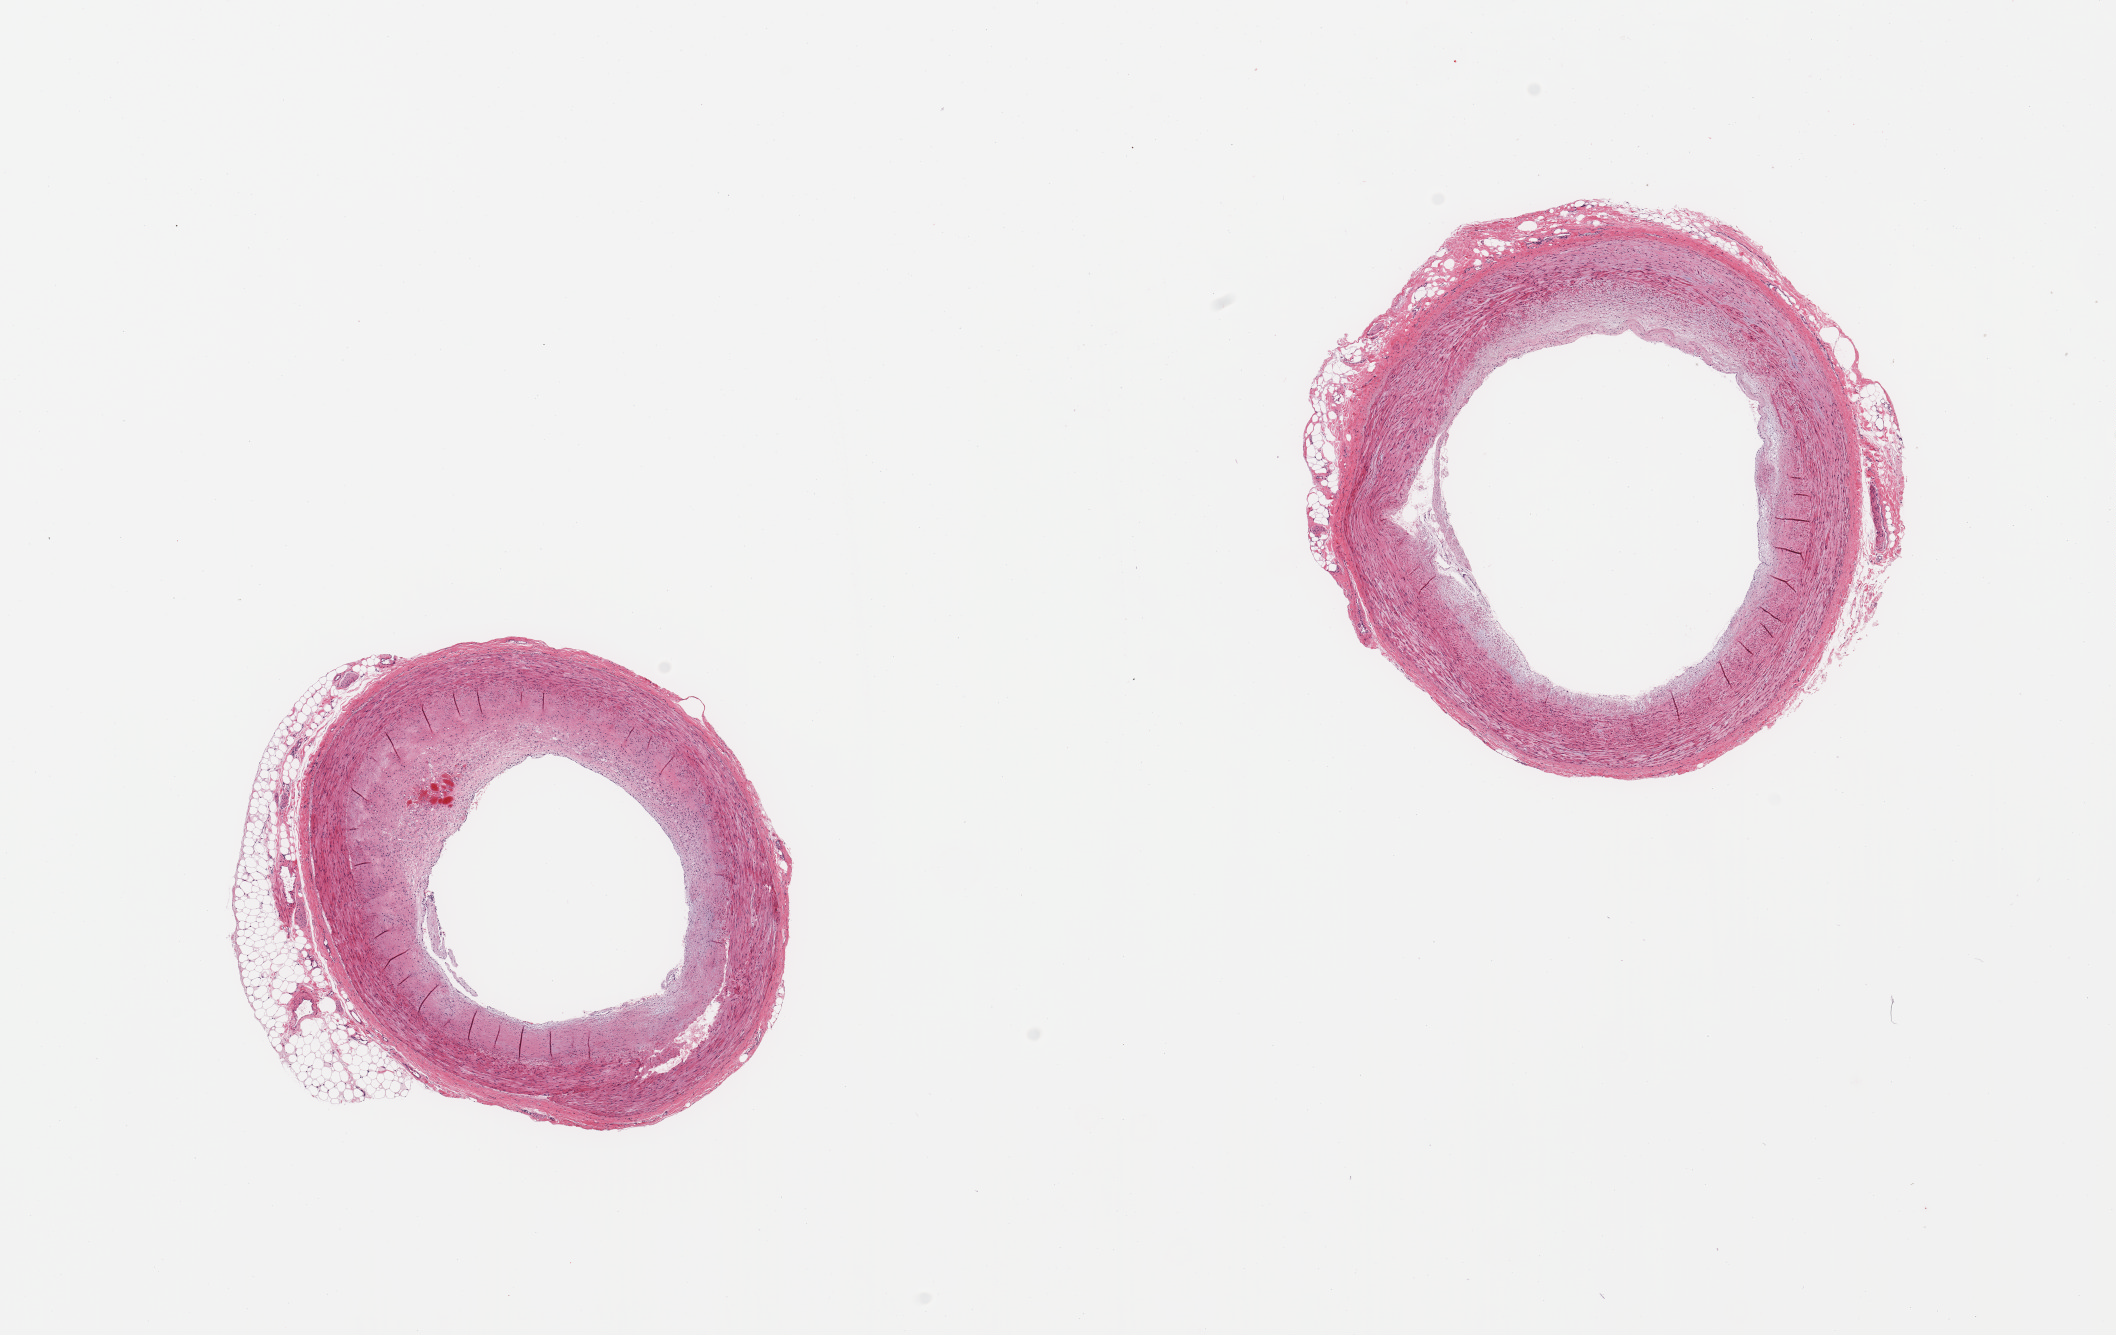
Digitized H&E-stained section, brightfield — low-resolution overview of the scanned area, about 16.7 x 10.6 mm, PAXgene-fixed paraffin-embedded (PFPE) section, target tissue: coronary artery, donor tissue sample.
Reviewer comment on this tissue sample: 2 pieces, ~15-20% occlusive atherosis; Trace adherent fat up to ~0.5mm.